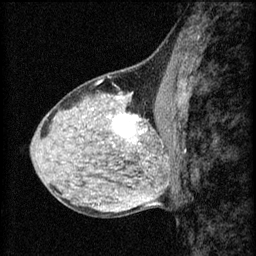
Breast MRI (dynamic contrast-enhanced), one sagittal slice. 3 images stored at this slice position (order not interpretable as contrast timing). 1.5 T. TE 4.2 ms, TR 8.2 ms. 2 mm slice thickness. 256 × 256 image matrix, field of view 180 × 180 mm. Female patient, age 40 years.
Structures marked on this image (semi-automatic segmentation, software-assisted and operator-edited):
- analysis volume of interest (the breast-tissue region the enhancement analysis was run in; not a lesion): bounding box (x1, y1, x2, y2) in pixels: (108, 108, 167, 159)
- tumour enhancement mask (voxels above the 70 % enhancement threshold inside the analysis volume of interest): (114, 114, 145, 145)